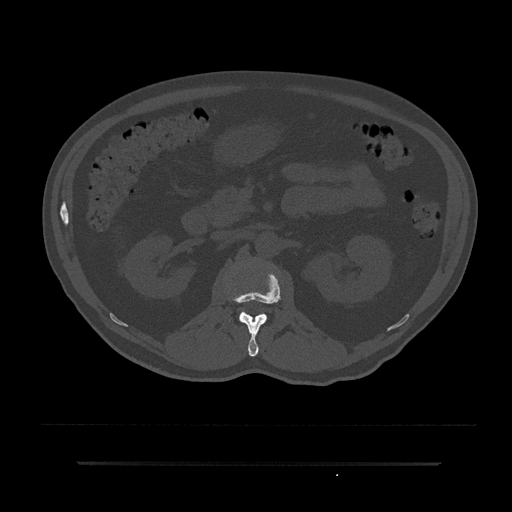
CT including the spine, one axial slice; position 121 of 797 along the scan axis; 120 kVp; bone window (W 1800 / L 400 HU); 512 × 512 image matrix, field of view 464 × 464 mm. Patient: male, 59 years. Case-level facts recorded for this patient, not image findings: primary cancer: bile ducts; vertebrae with lytic lesions (as recorded): T10.
Annotated regions visible in this slice (semi-automatically segmented with operator editing):
- L1 vertebra: bounding box <229,271,282,357> (left, top, right, bottom; pixels)
- L2 vertebra: <241,312,267,318>